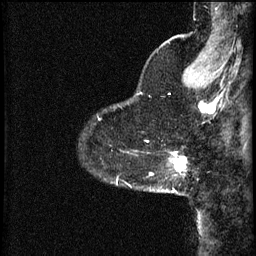
Breast MRI (dynamic contrast-enhanced), one sagittal slice; 3 images stored at this slice position (order not interpretable as contrast timing); 1.5 T; TE 4.2 ms, TR 8.2 ms; 2 mm slice thickness; 256 × 256 image matrix, field of view 200 × 200 mm. Patient: female, 37 years.
Structures marked on this image (semi-automatically segmented with operator editing):
- analysis volume of interest (the breast-tissue region the enhancement analysis was run in; not a lesion): bounding box (x1, y1, x2, y2) in pixels: (148, 152, 187, 195)
- tumour enhancement mask (voxels above the 70 % enhancement threshold inside the analysis volume of interest): (174, 152, 187, 173)